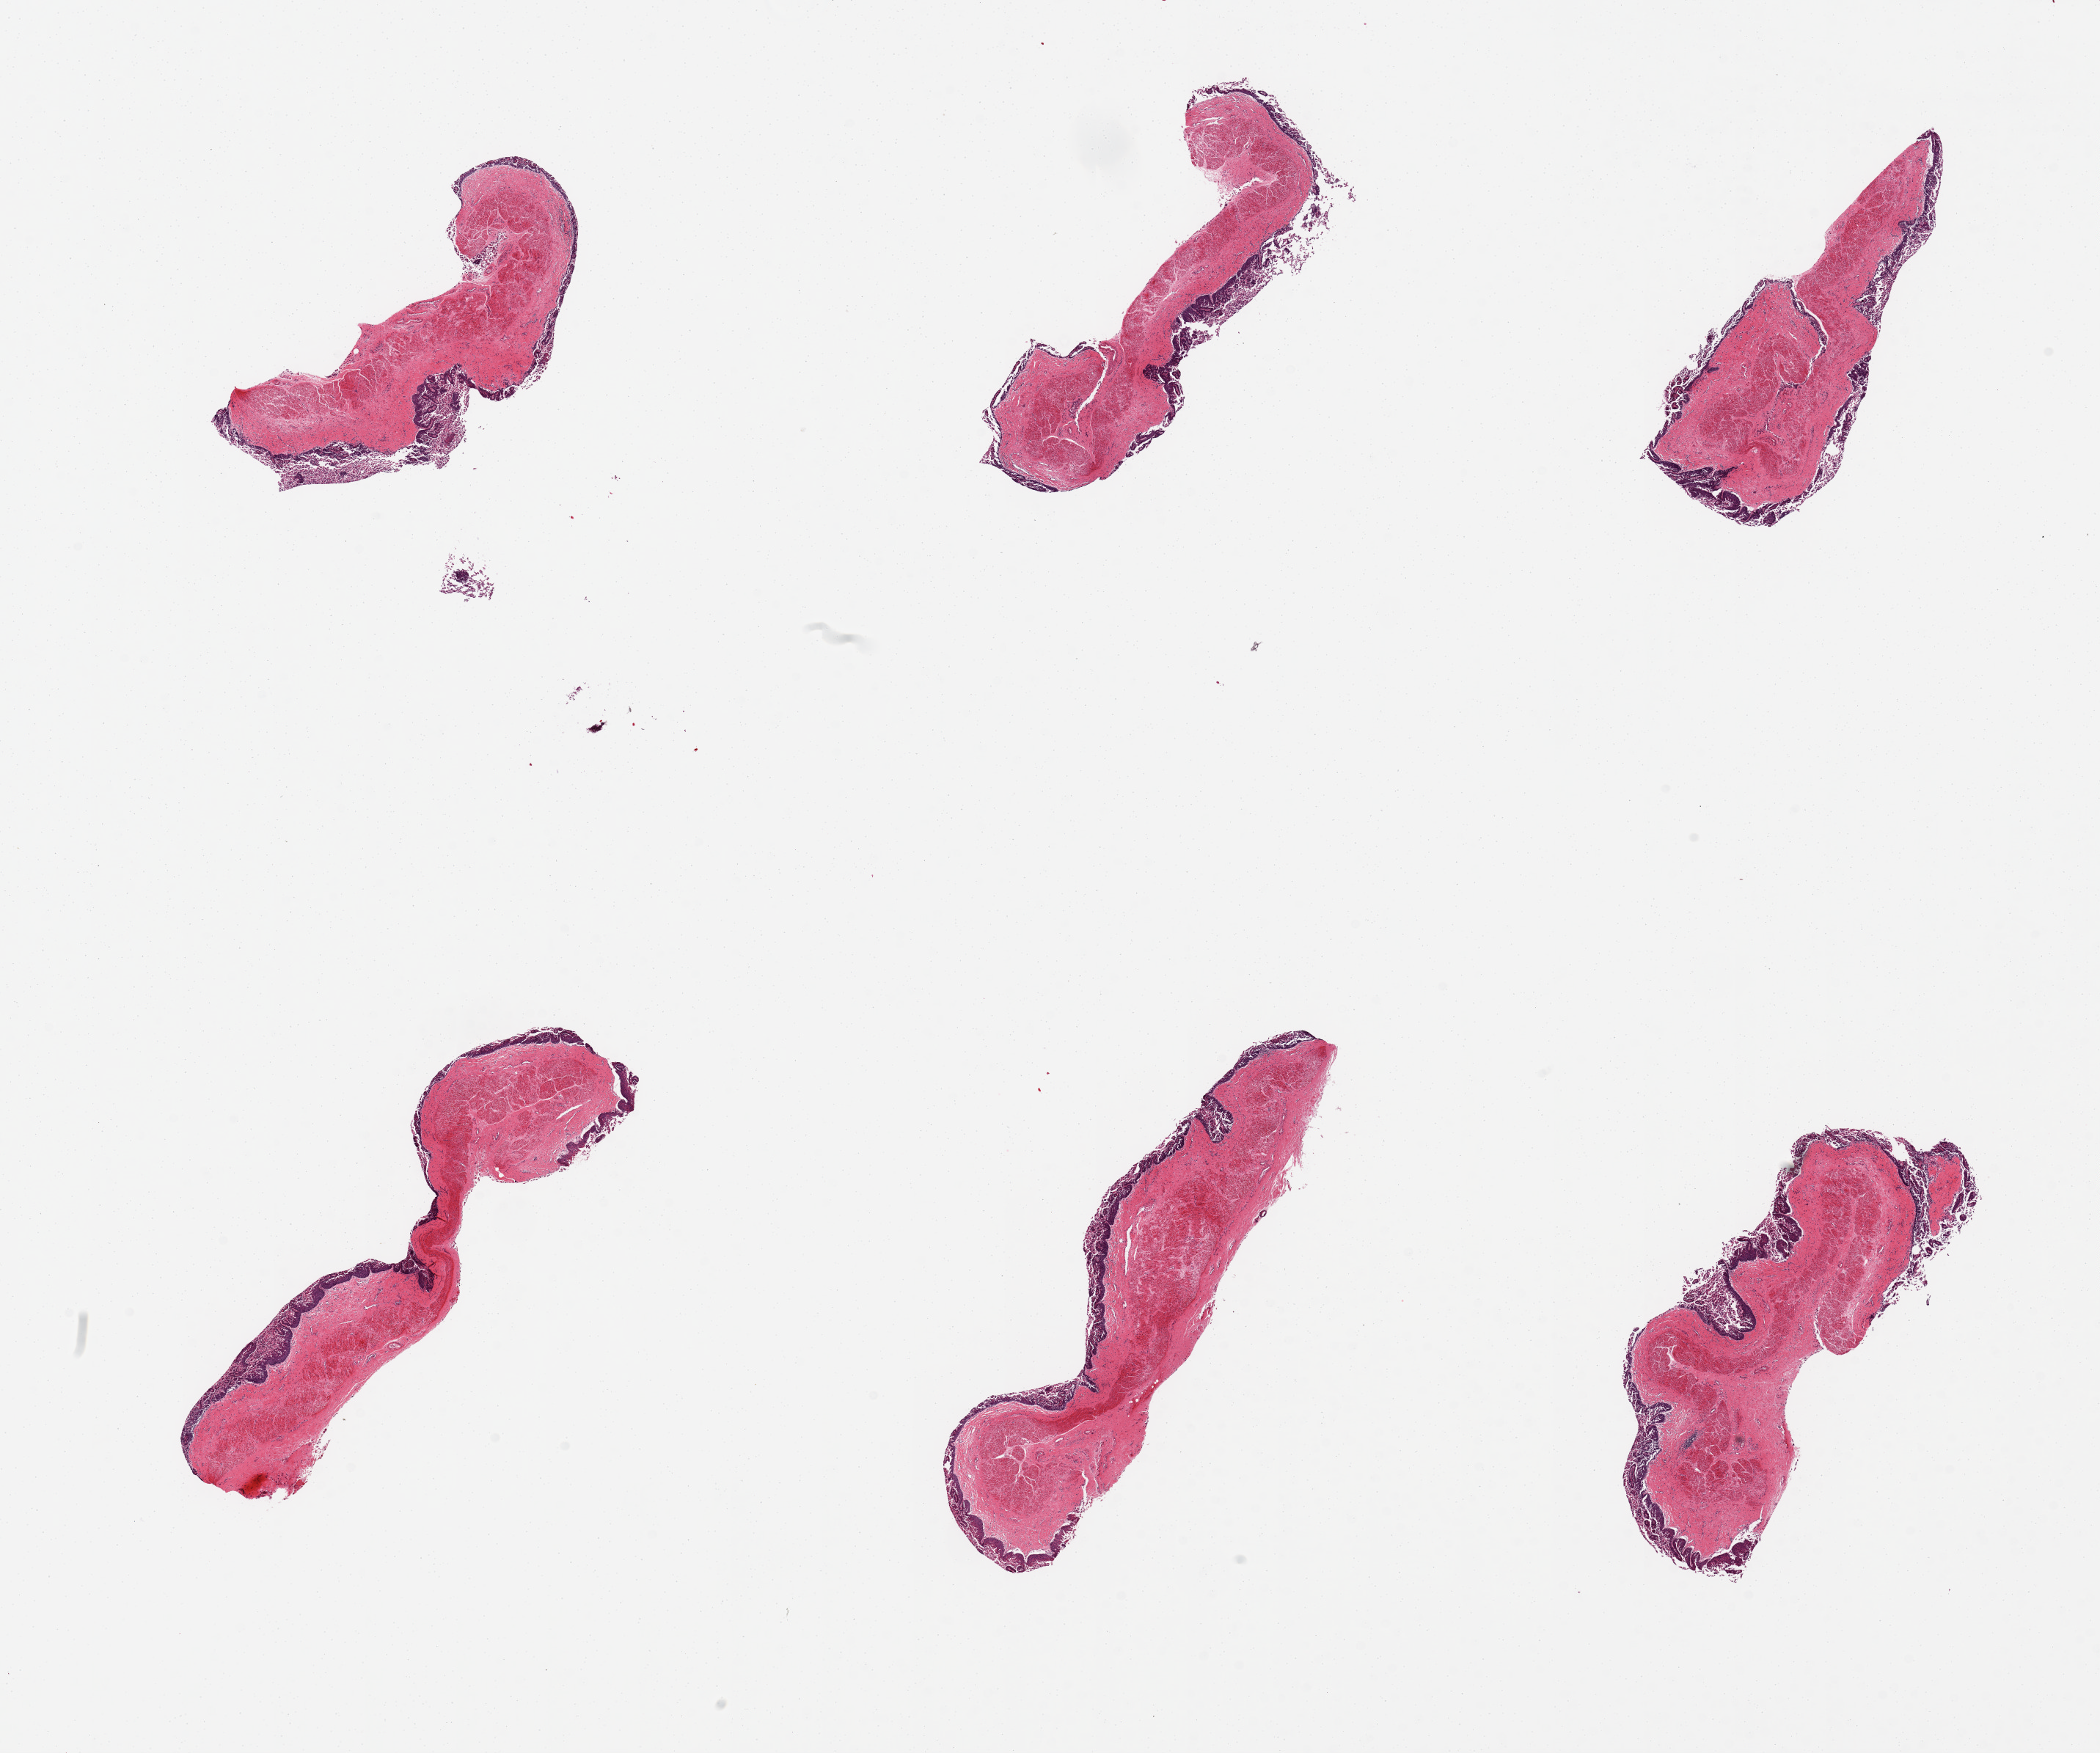
Hematoxylin and eosin (H&E) whole-slide image, brightfield — shown as a low-resolution overview of the whole scanned area (about 22.6 x 18.9 mm, slide scanned at 20x). PAXgene-fixed, paraffin-embedded tissue. Target tissue: esophageal mucous membrane. Donor tissue sample. Male donor.
Pathologist's review note for this sample: 6 pieces, junctional mucosa, badly autolyzed.